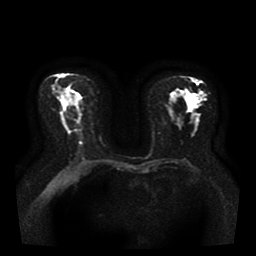
Breast MRI, one axial slice; slice 19 of 36 in the series (ordered by position); diffusion-weighted series; image 2 of 4 stored at this slice position (different b-values; order by instance number); 1.5 T; 256 × 256 image matrix. Female patient.
Outlined on this slice (outlined manually by an expert reader):
- tumour on diffusion-weighted imaging: box from (x=191, y=96) to (x=200, y=108) px